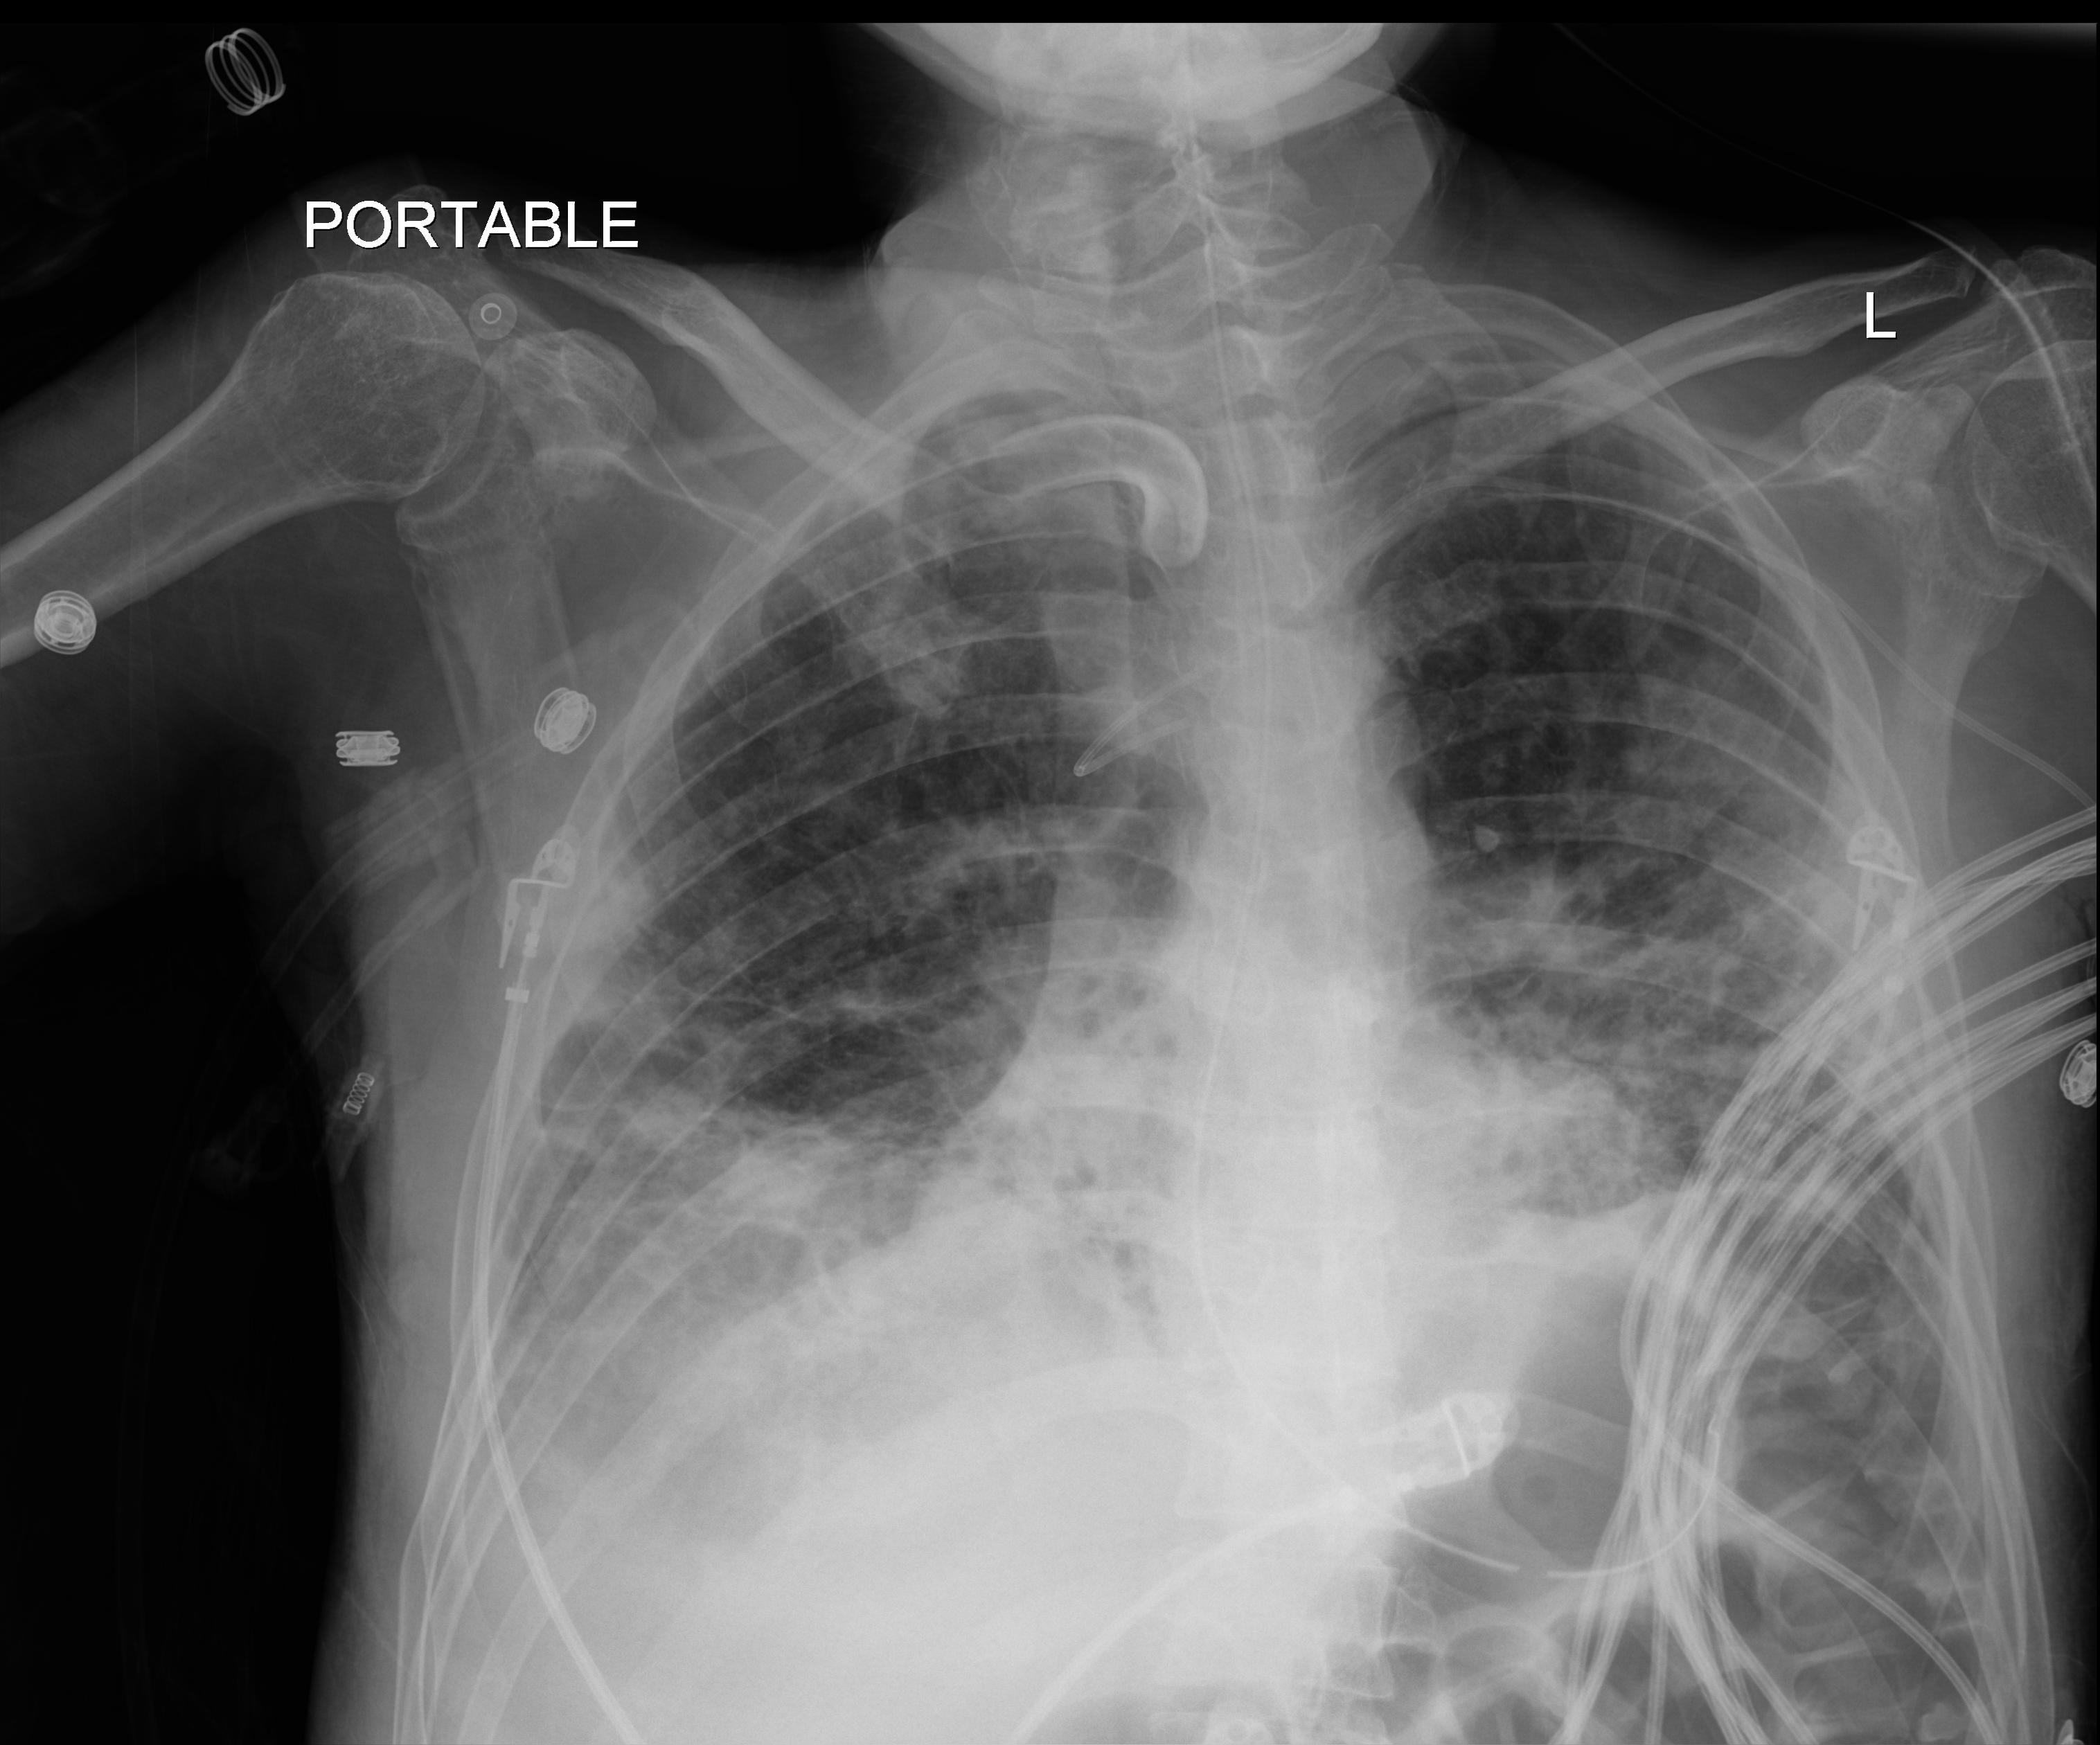
Chest X-ray (portable), anteroposterior (AP) projection. Male patient hospitalised with COVID-19, age 18–59 years.
From the hospital-stay record, not from the radiograph (when in the stay this image was taken is not recorded):
- chronic kidney disease (admission record): no
- hypertension (admission record): yes
- COPD (admission record): no